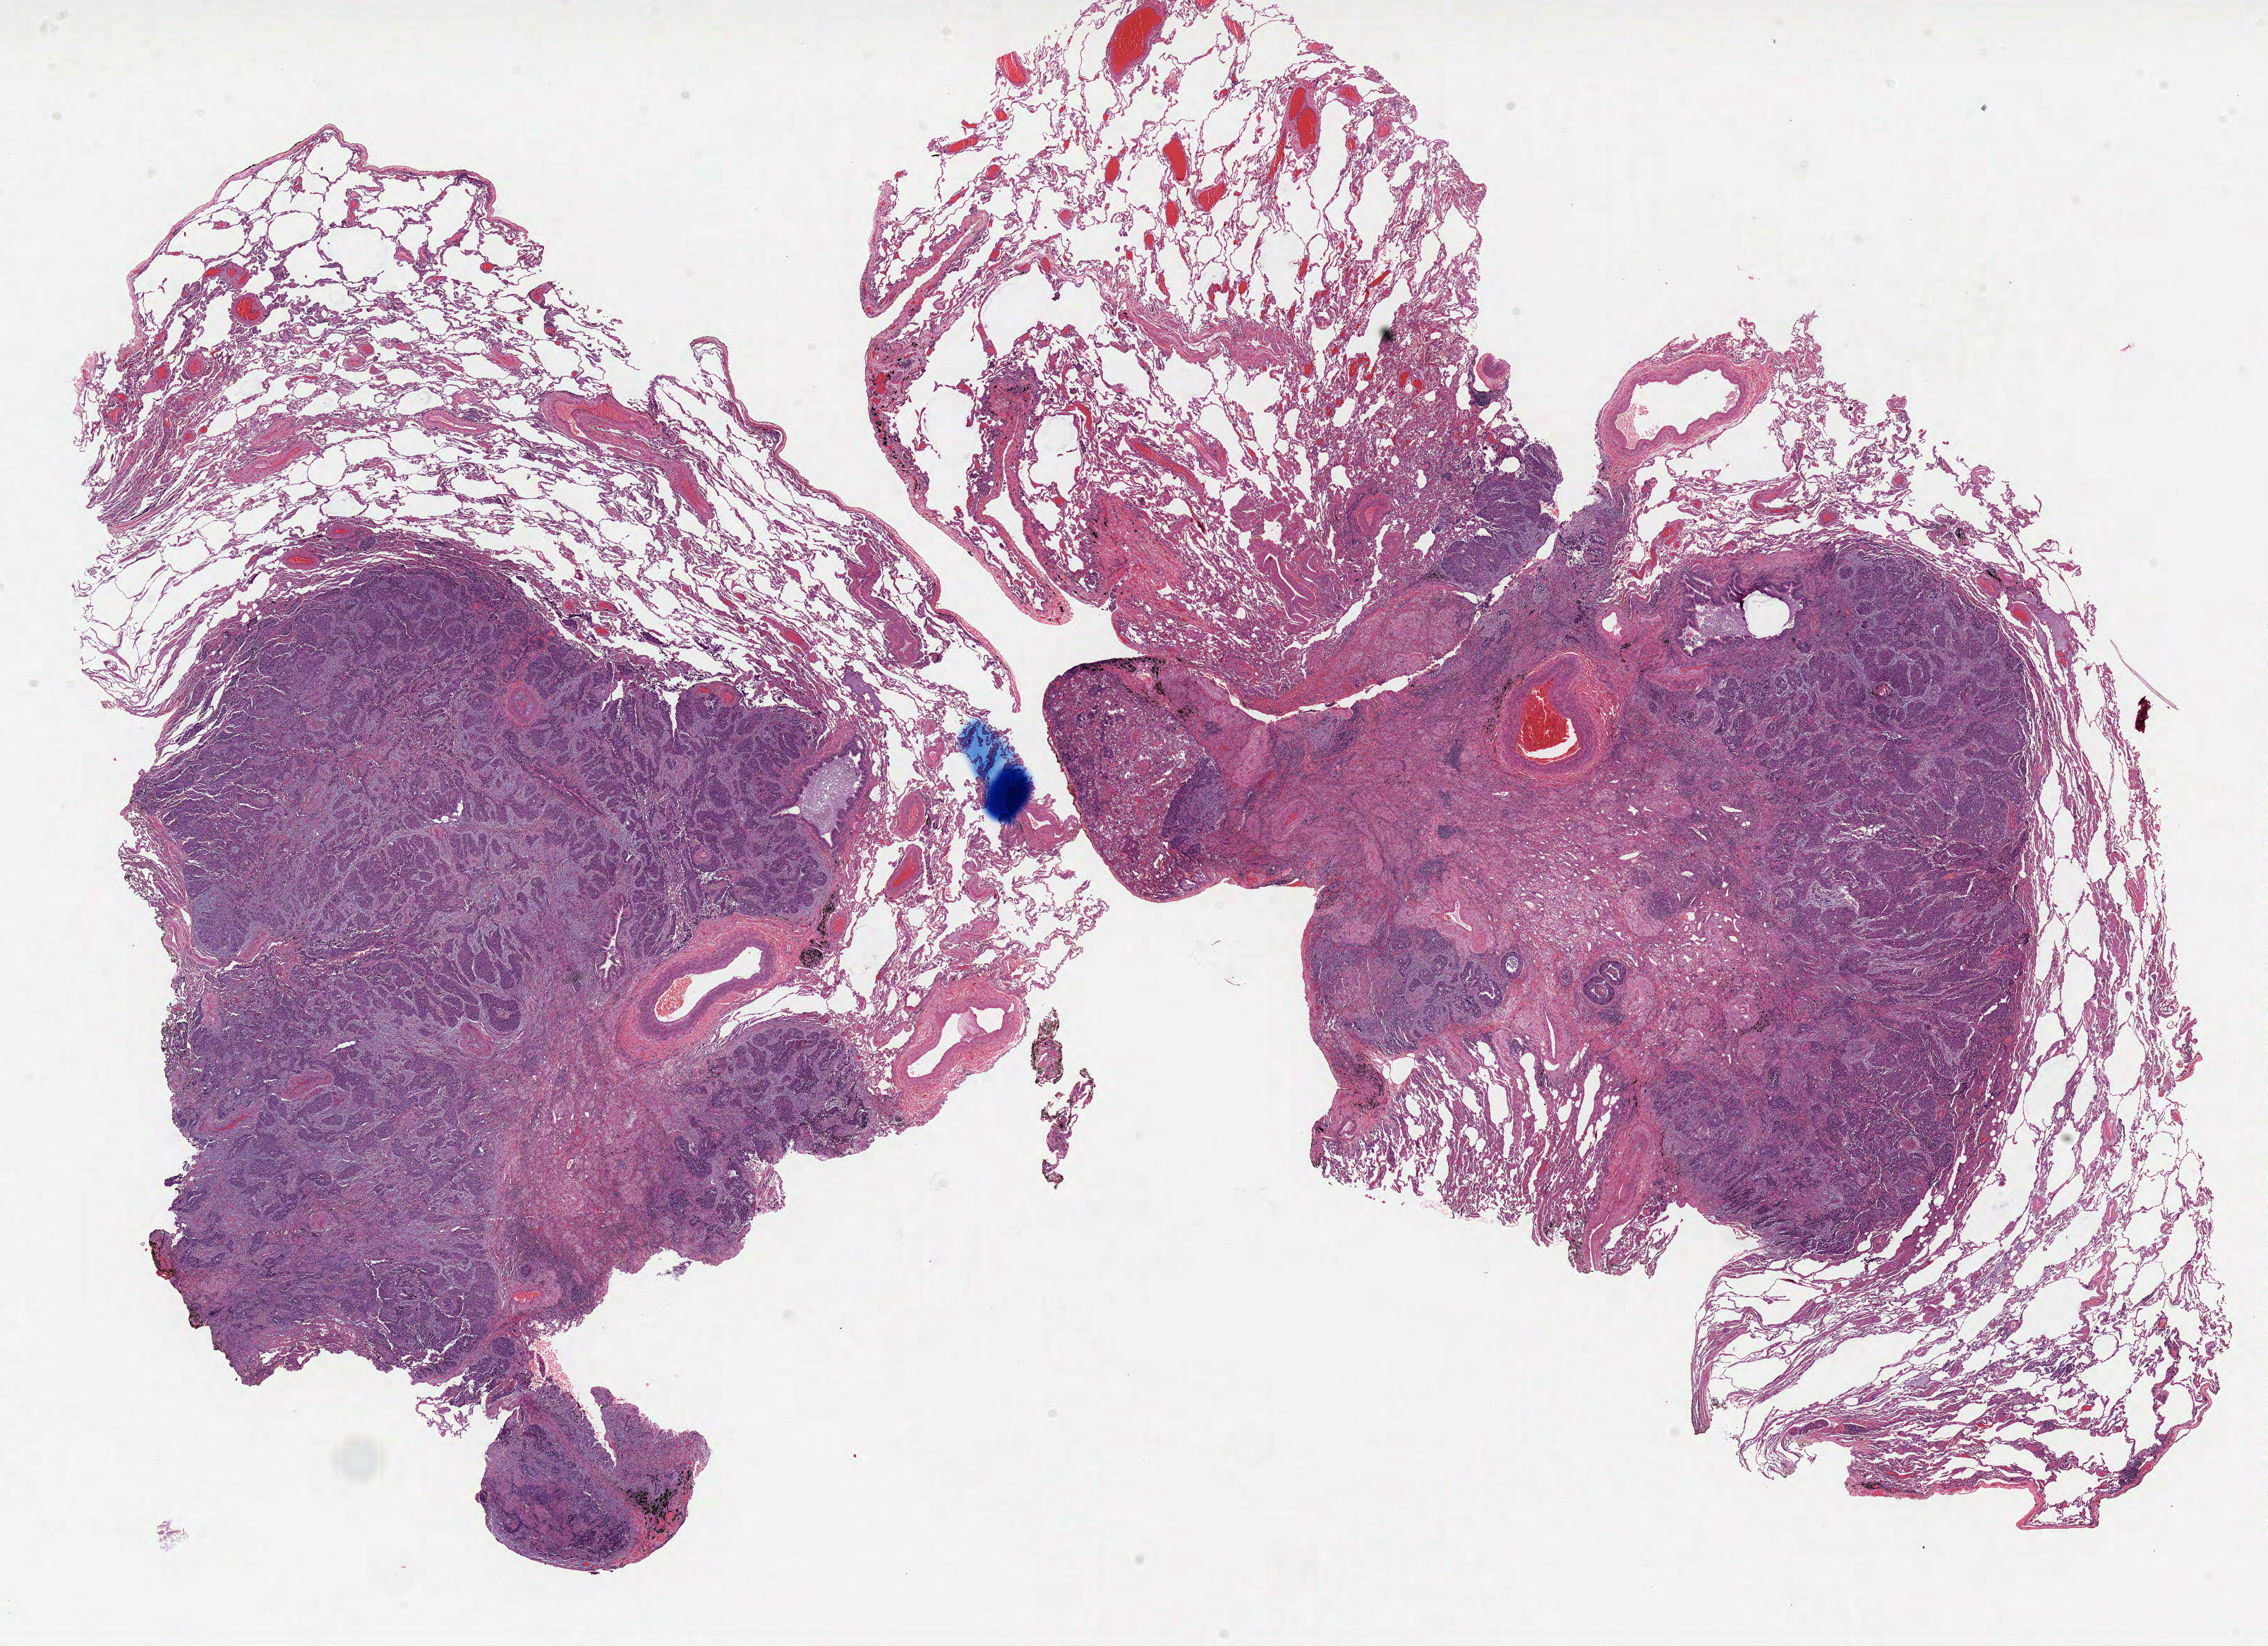
Hematoxylin and eosin (H&E) stained whole-slide image — low-resolution overview of the scanned area, about 25.9 x 18.8 mm (acquisition: 20x scan); formalin-fixed paraffin-embedded (FFPE) diagnostic section; lung, primary tumour sample. Male patient; age at initial diagnosis 73 years.
• diagnosis: Squamous cell carcinoma, NOS (upper lobe, lung)
• AJCC pathologic stage: IB